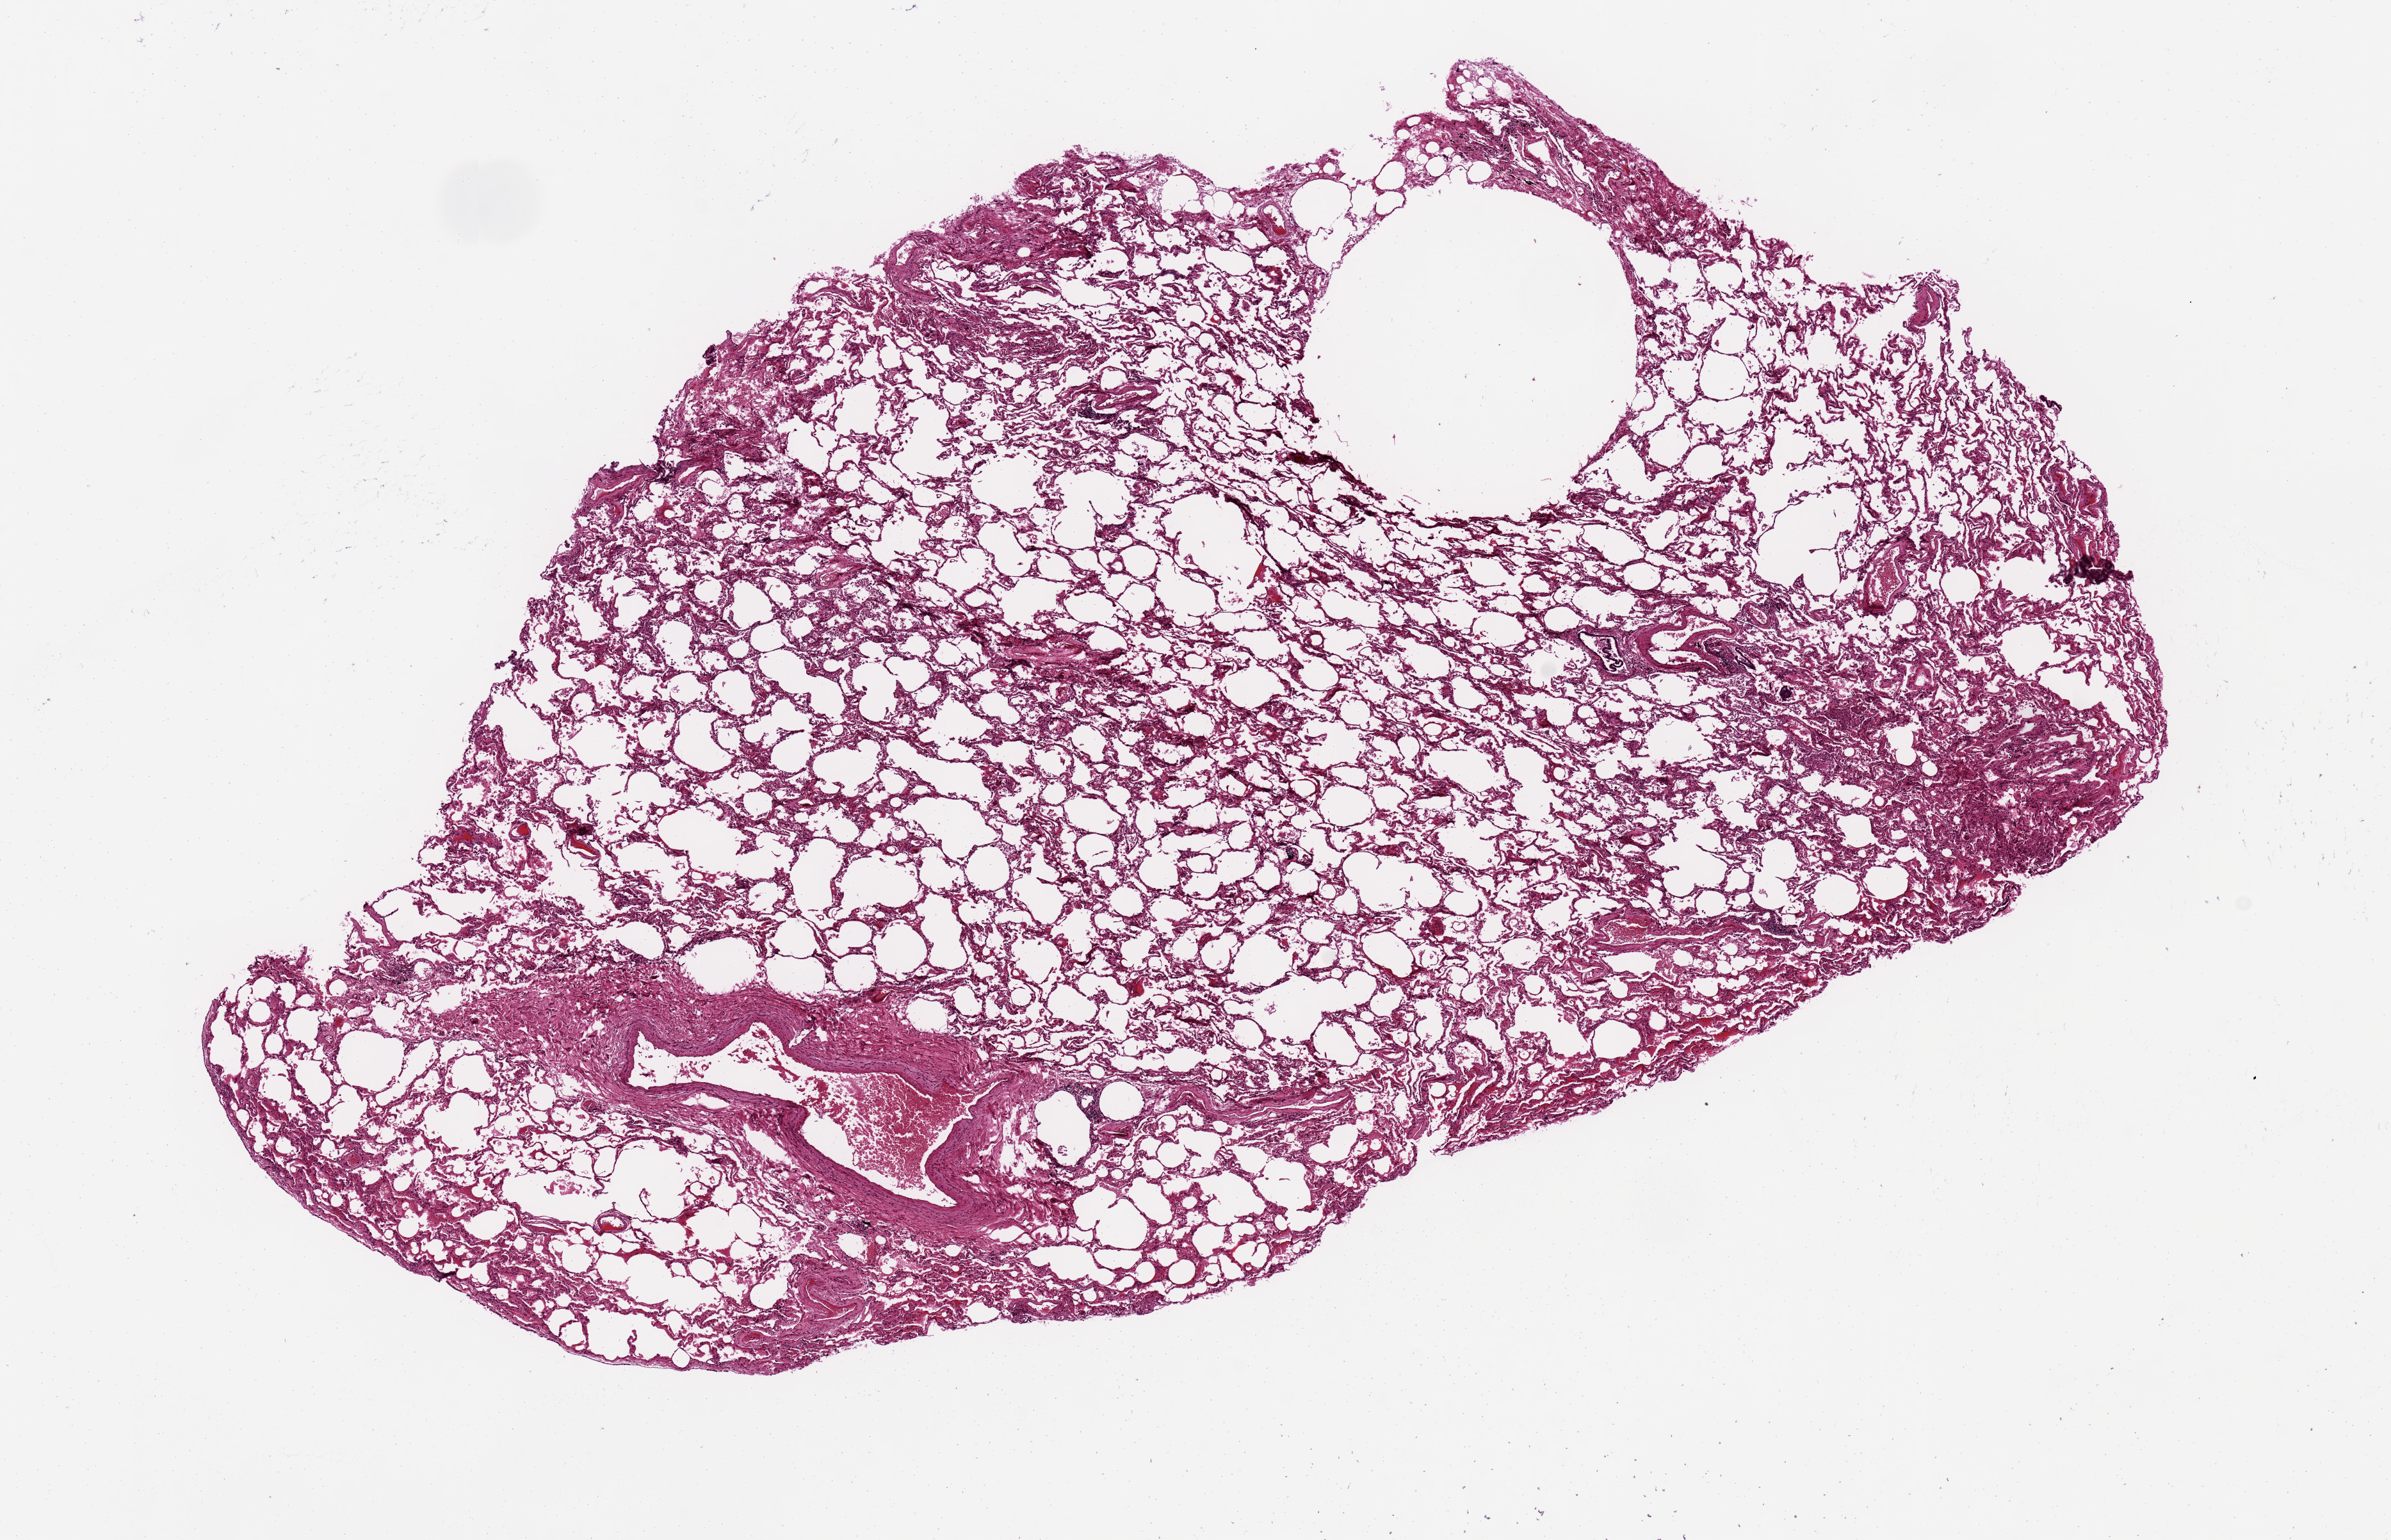
Whole-slide image, H&E stain, shown as a low-resolution overview of the whole scanned area (about 14.8 x 9.5 mm, from a 20x scan), PAXgene-fixed, paraffin-embedded tissue, section of lung (target tissue), tissue donor sample.
Review note (as recorded): 10x6 mm; 2 mm defect, possible fixation artifact.